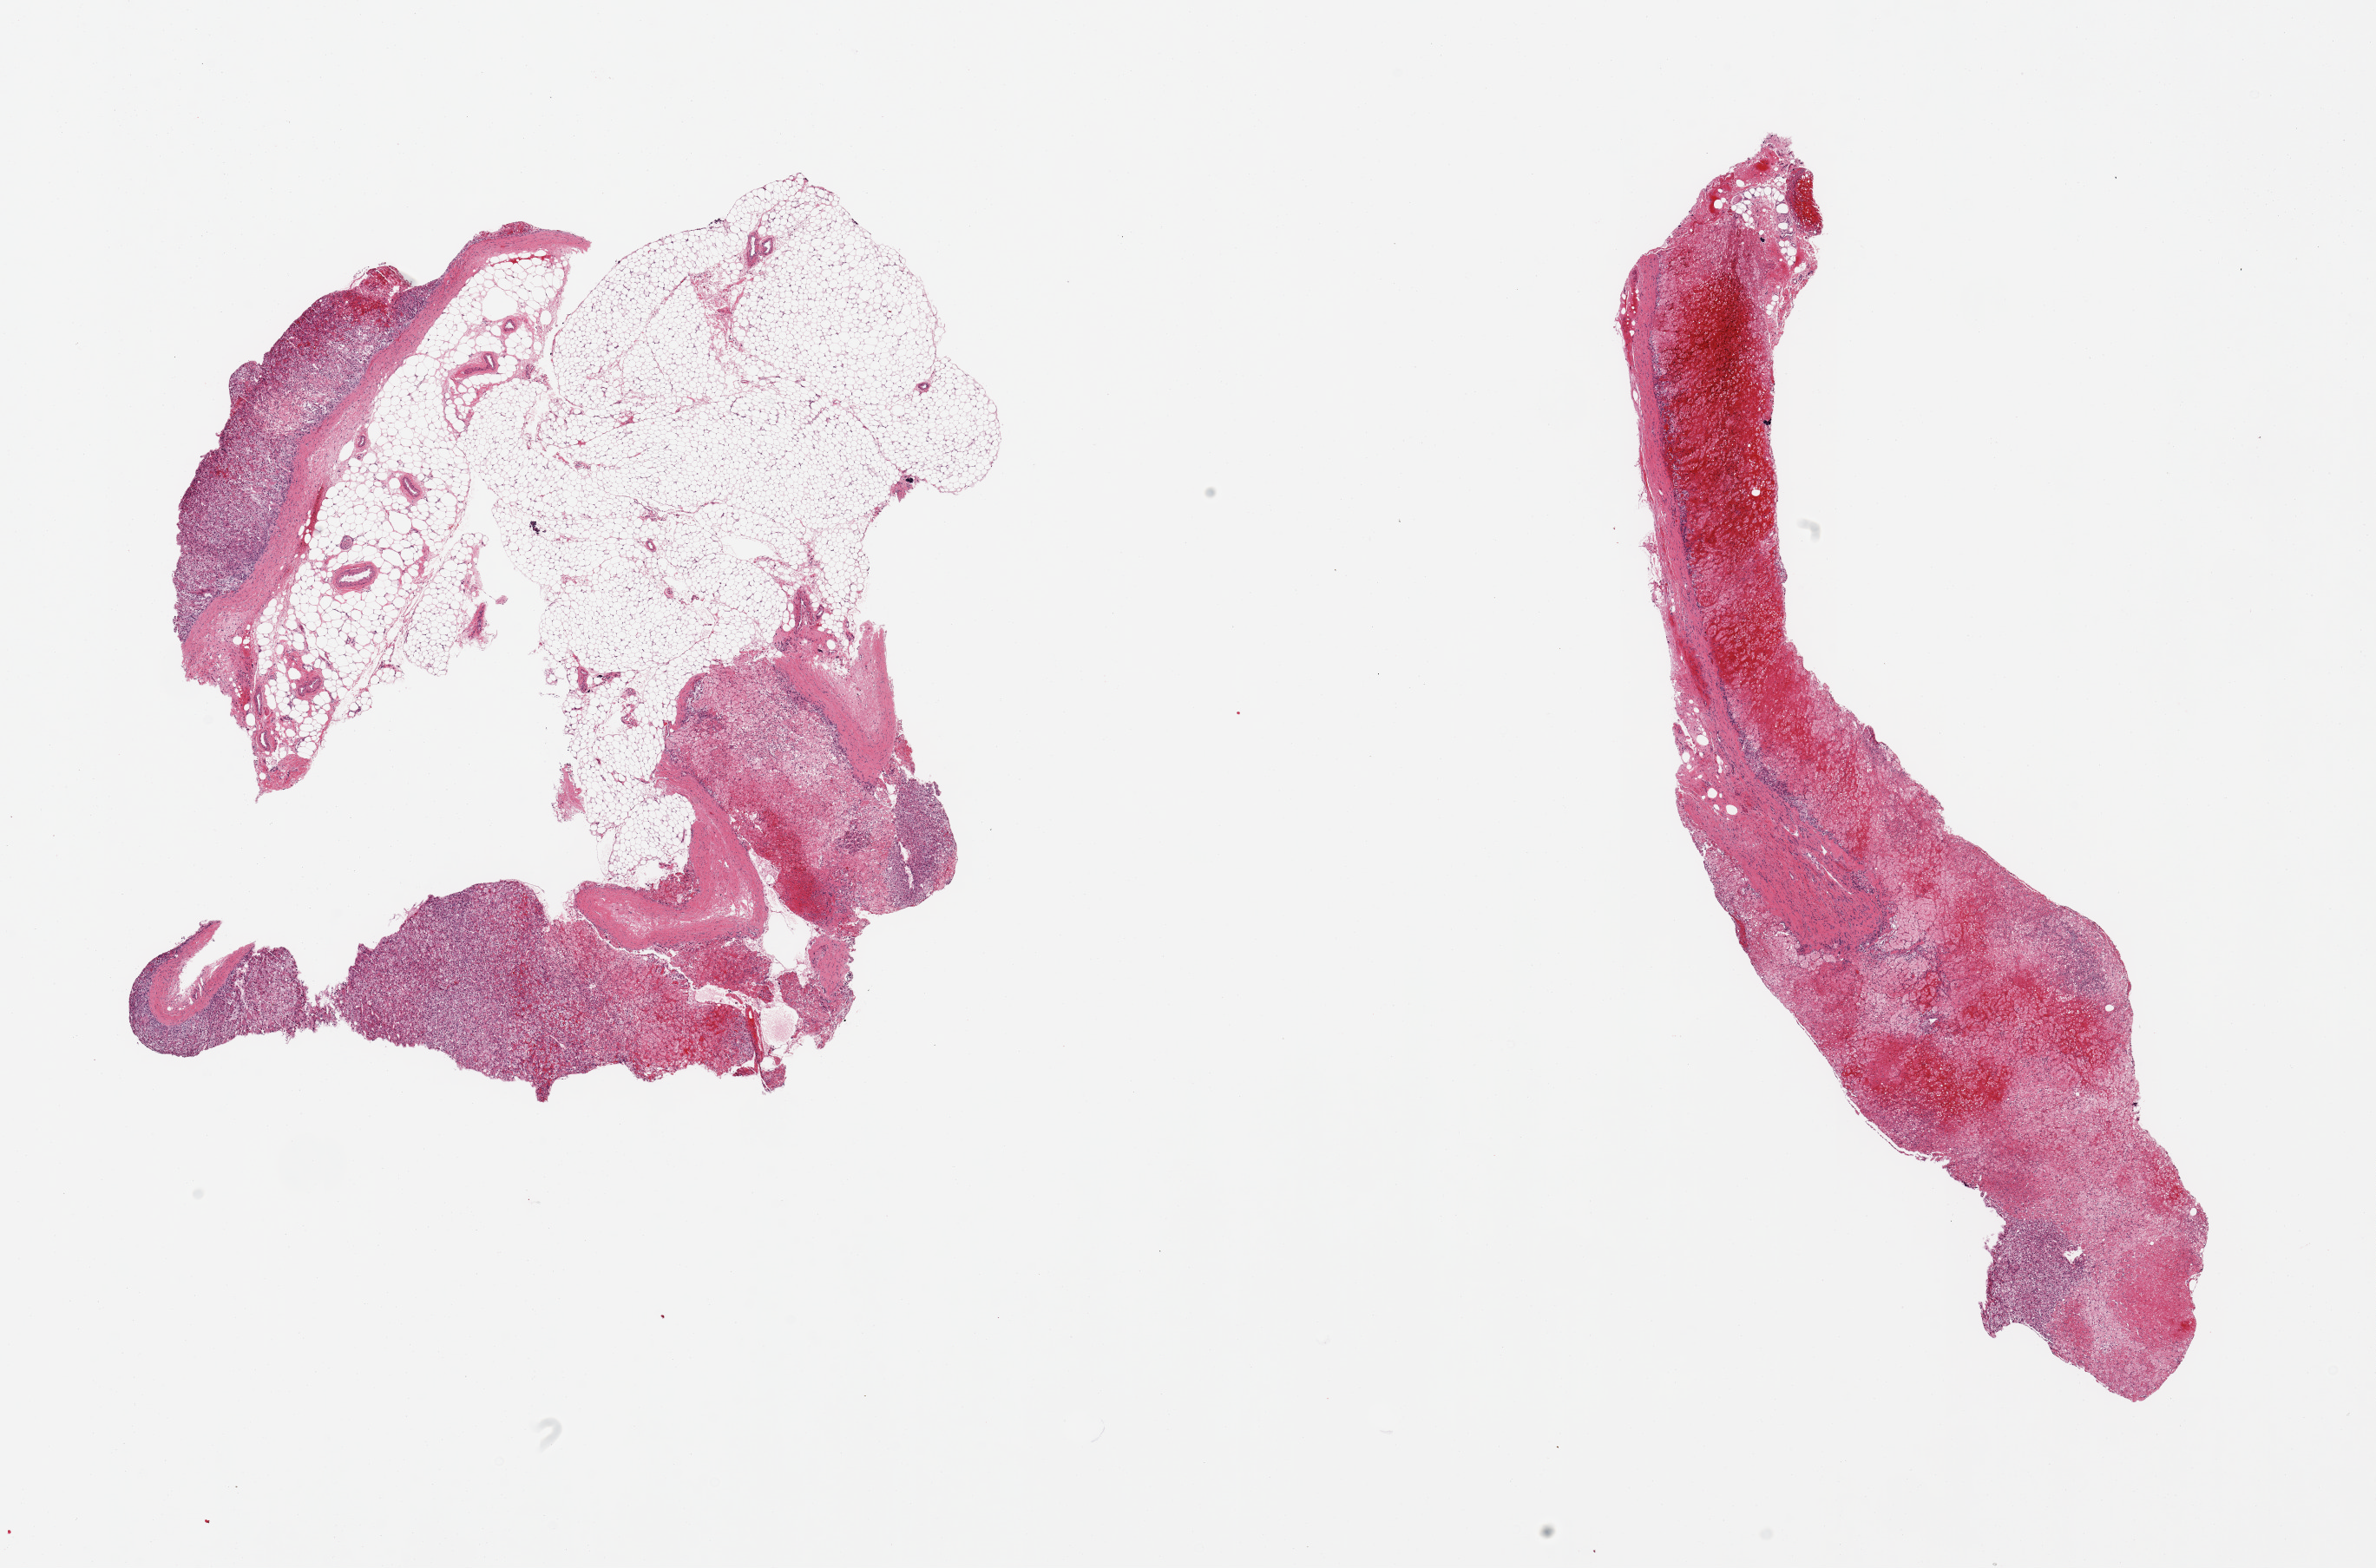
Digitized haematoxylin and eosin-stained section, brightfield, shown as a low-resolution overview of the whole scanned area (about 21.7 x 14.3 mm), PAXgene-fixed, paraffin-embedded tissue, section of adrenal gland (target tissue), tissue donor sample. Donor: female.
Reviewer comment on this tissue sample: 2 pieces, ~40% adherent/interstitial fat; patchy congestion/hemorrhage.